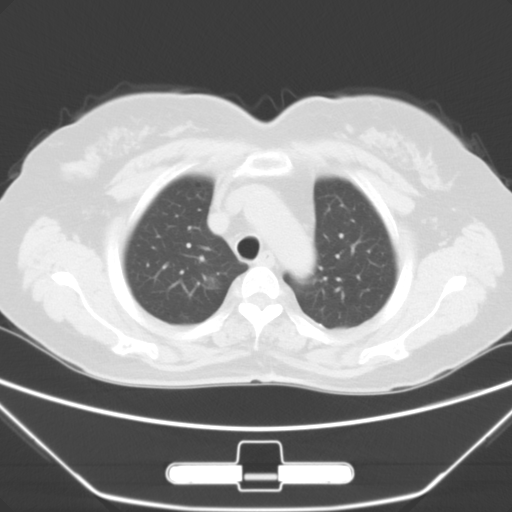
Chest CT, one axial slice. Position 45 of 55 along the scan axis. 120 kVp. Lung window (W 1500 / L -600 HU). 512 × 512 image matrix, field of view 356 × 356 mm. Patient: female, 63 years. From the clinical record (not read from this slice): clinical TNM (as recorded): T1a N0 M0.
Annotated regions visible in this slice (rectangle marked by the reading radiologist):
- lung tumour (recorded histology: adenocarcinoma): bounding box (x1, y1, x2, y2) in pixels: (194, 264, 225, 300)